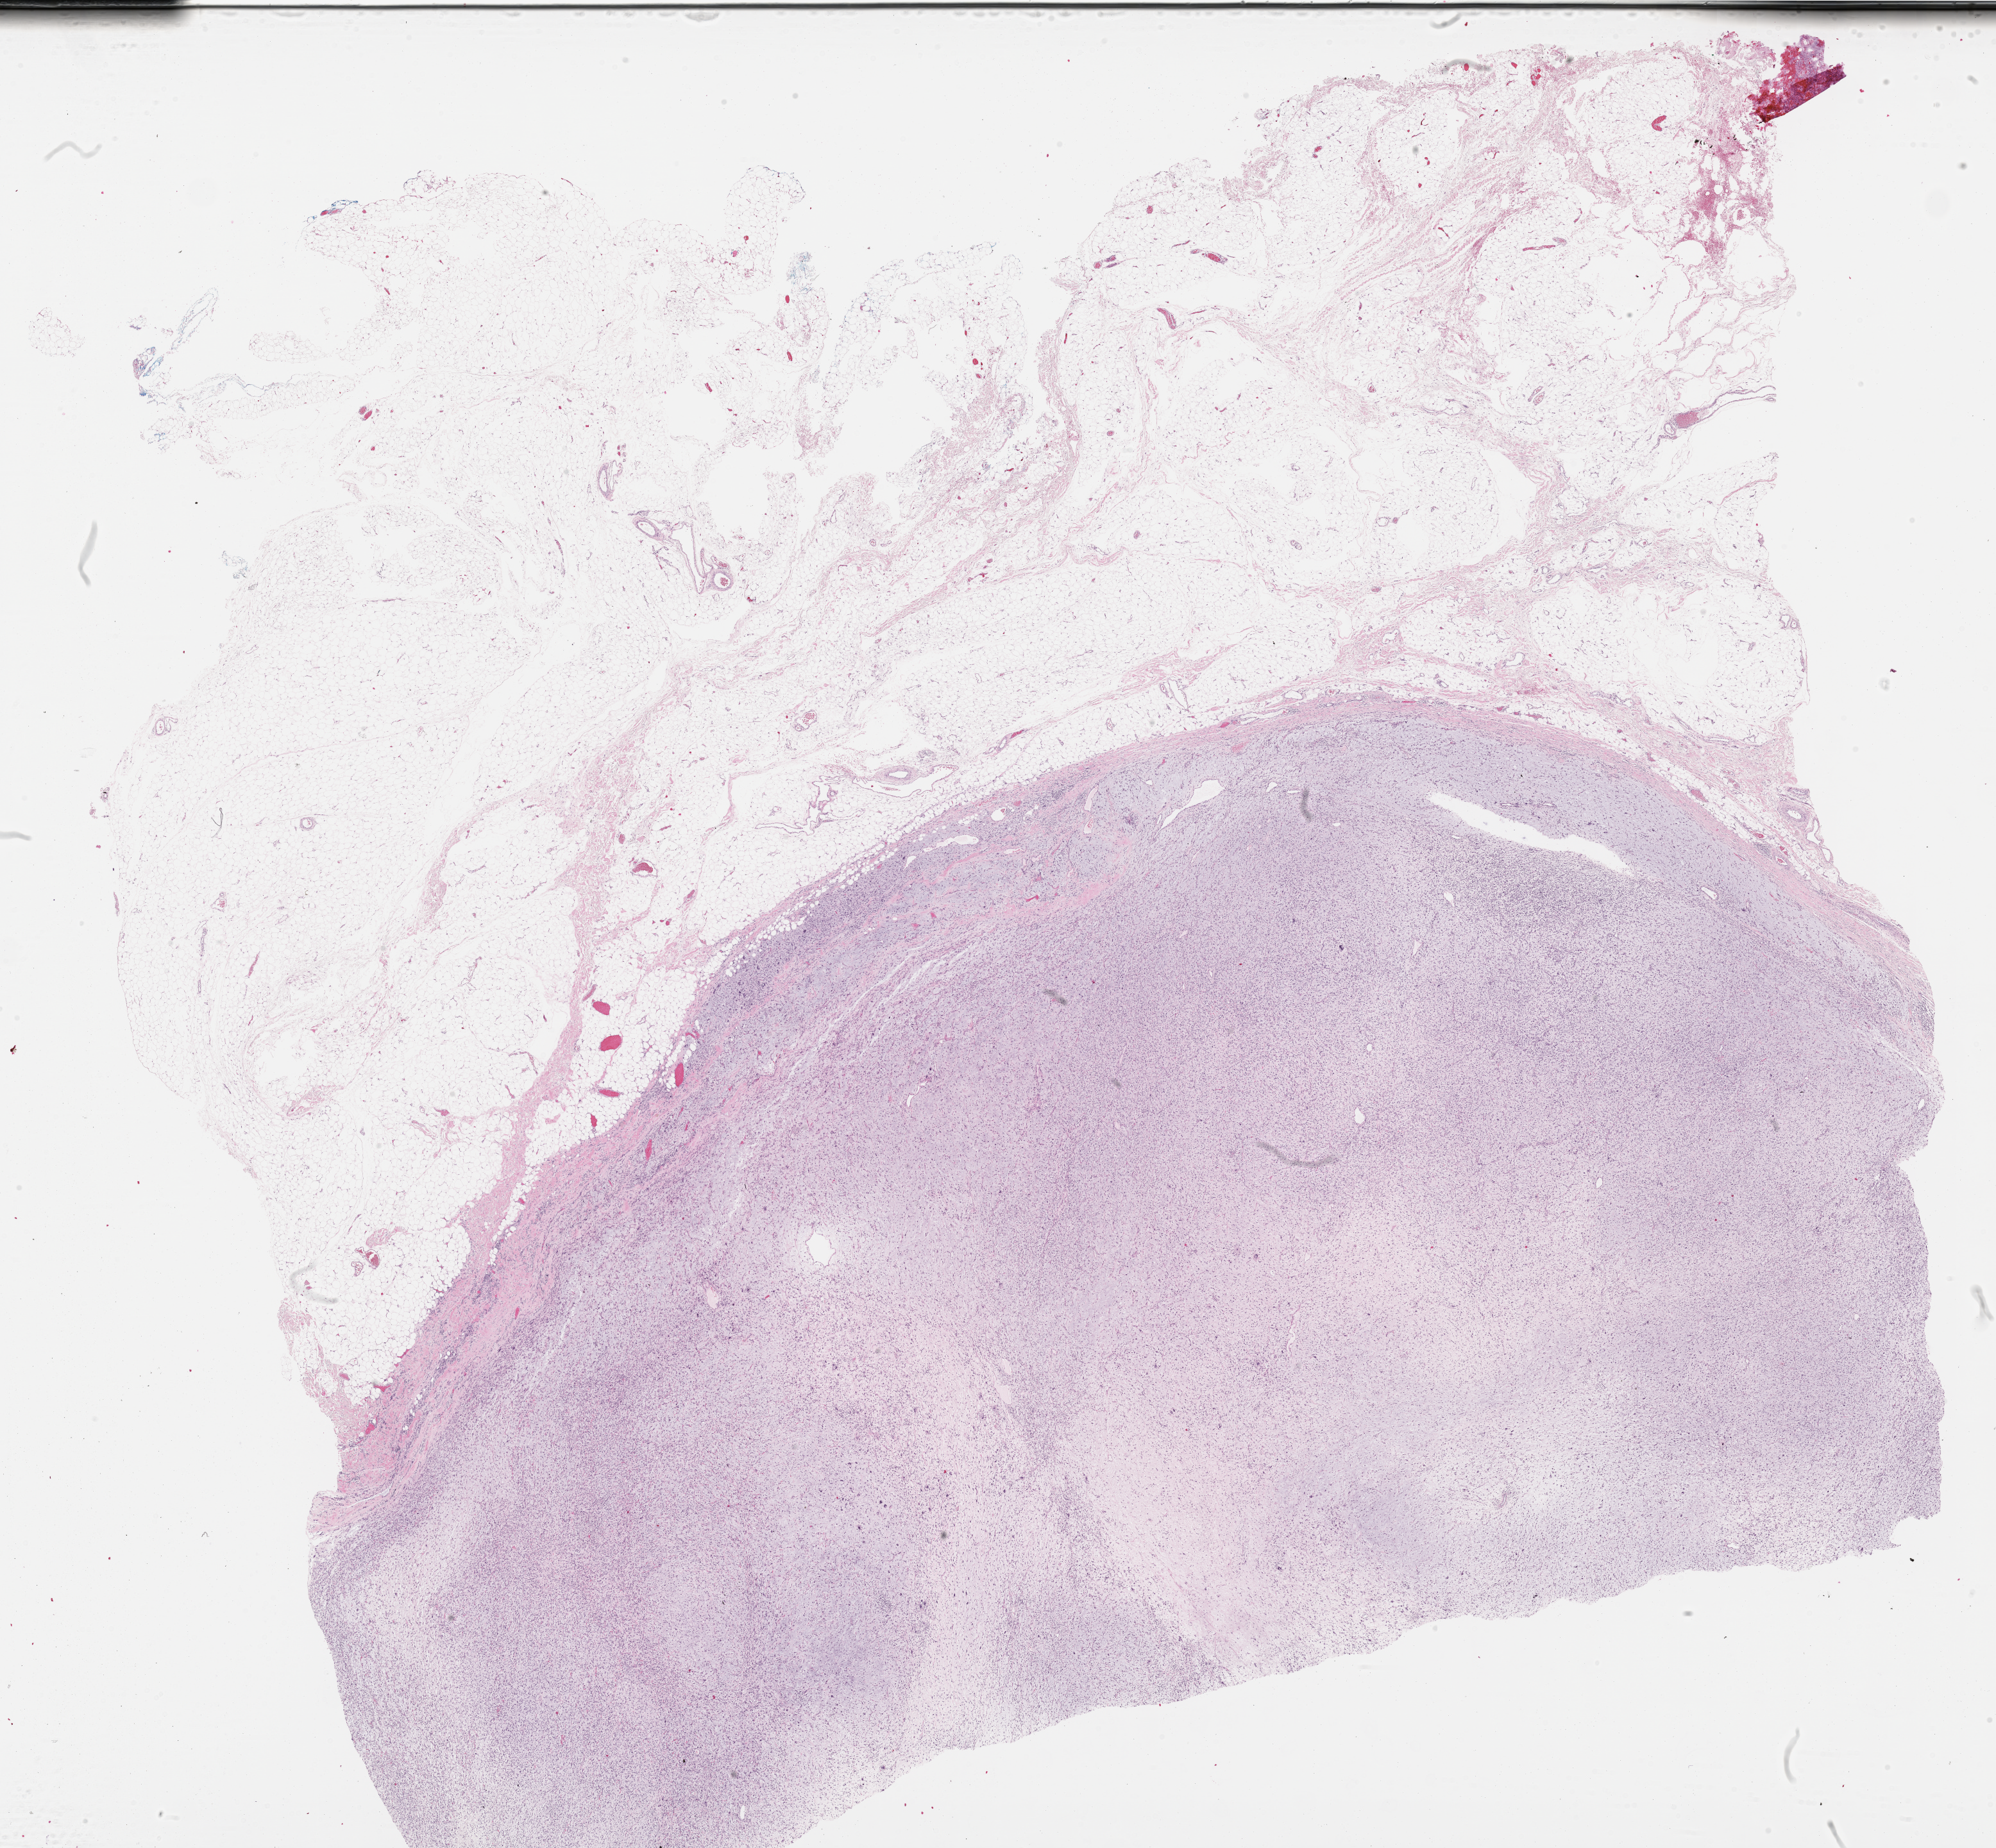
Digitized Hematoxylin and eosin (H&E) stained tissue section (whole slide) — a low-resolution overview of the entire scanned area, about 25.2 x 23.3 mm. Formalin-fixed paraffin-embedded (FFPE) diagnostic section. Connective, subcutaneous and other soft tissues, primary tumour sample. Female patient; age at initial diagnosis 50 years.
* histologic diagnosis: Fibromyxosarcoma (connective, subcutaneous and other soft tissues of thorax)